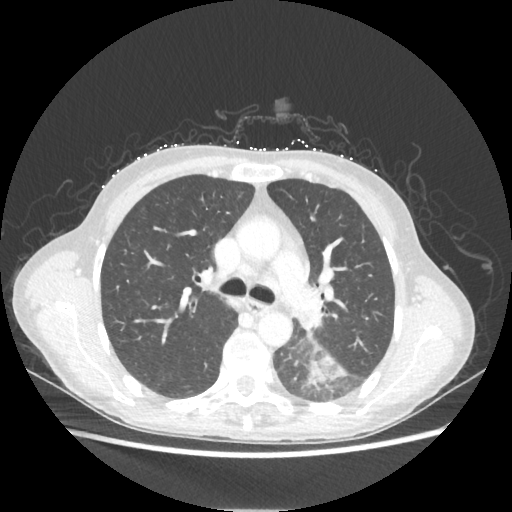
Chest CT, one axial slice; slice 141 of 221 in the series (ordered by position); reconstruction kernel STANDARD; 80 kVp; lung window (W 1500 / L -600 HU); 512 × 512 image matrix, field of view 360 × 360 mm. Patient: female, 53 years. From the clinical record (not read from this slice): clinical TNM (as recorded): T3 N0 M0.
Outlined on this slice (bounding box drawn by a radiologist):
- lung tumour (recorded histology: adenocarcinoma): box from (x=308, y=353) to (x=344, y=386) px